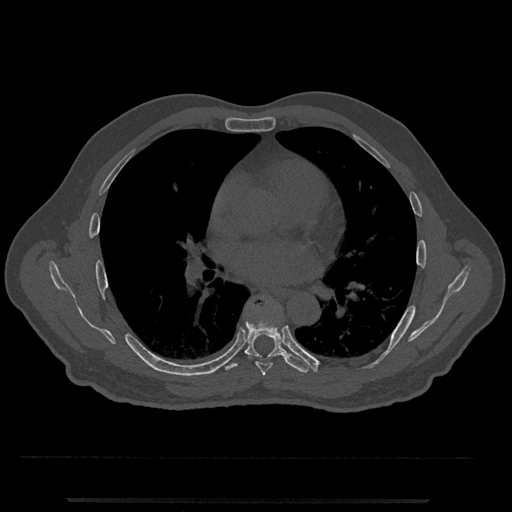
CT including the spine, one axial slice. Slice 709 of 797 in the series (ordered by position). 120 kVp. Bone window (W 1800 / L 400 HU). 0.5 mm slice thickness. 512 × 512 image matrix. Male patient, age 63 years. From the clinical record (not read from this slice): primary cancer: prostate.
Outlined on this slice (semi-automatic segmentation, software-assisted and operator-edited):
- T6 vertebra: bounding box [x1, y1, x2, y2] px = [256, 362, 273, 376]
- T7 vertebra: [221, 299, 317, 373]